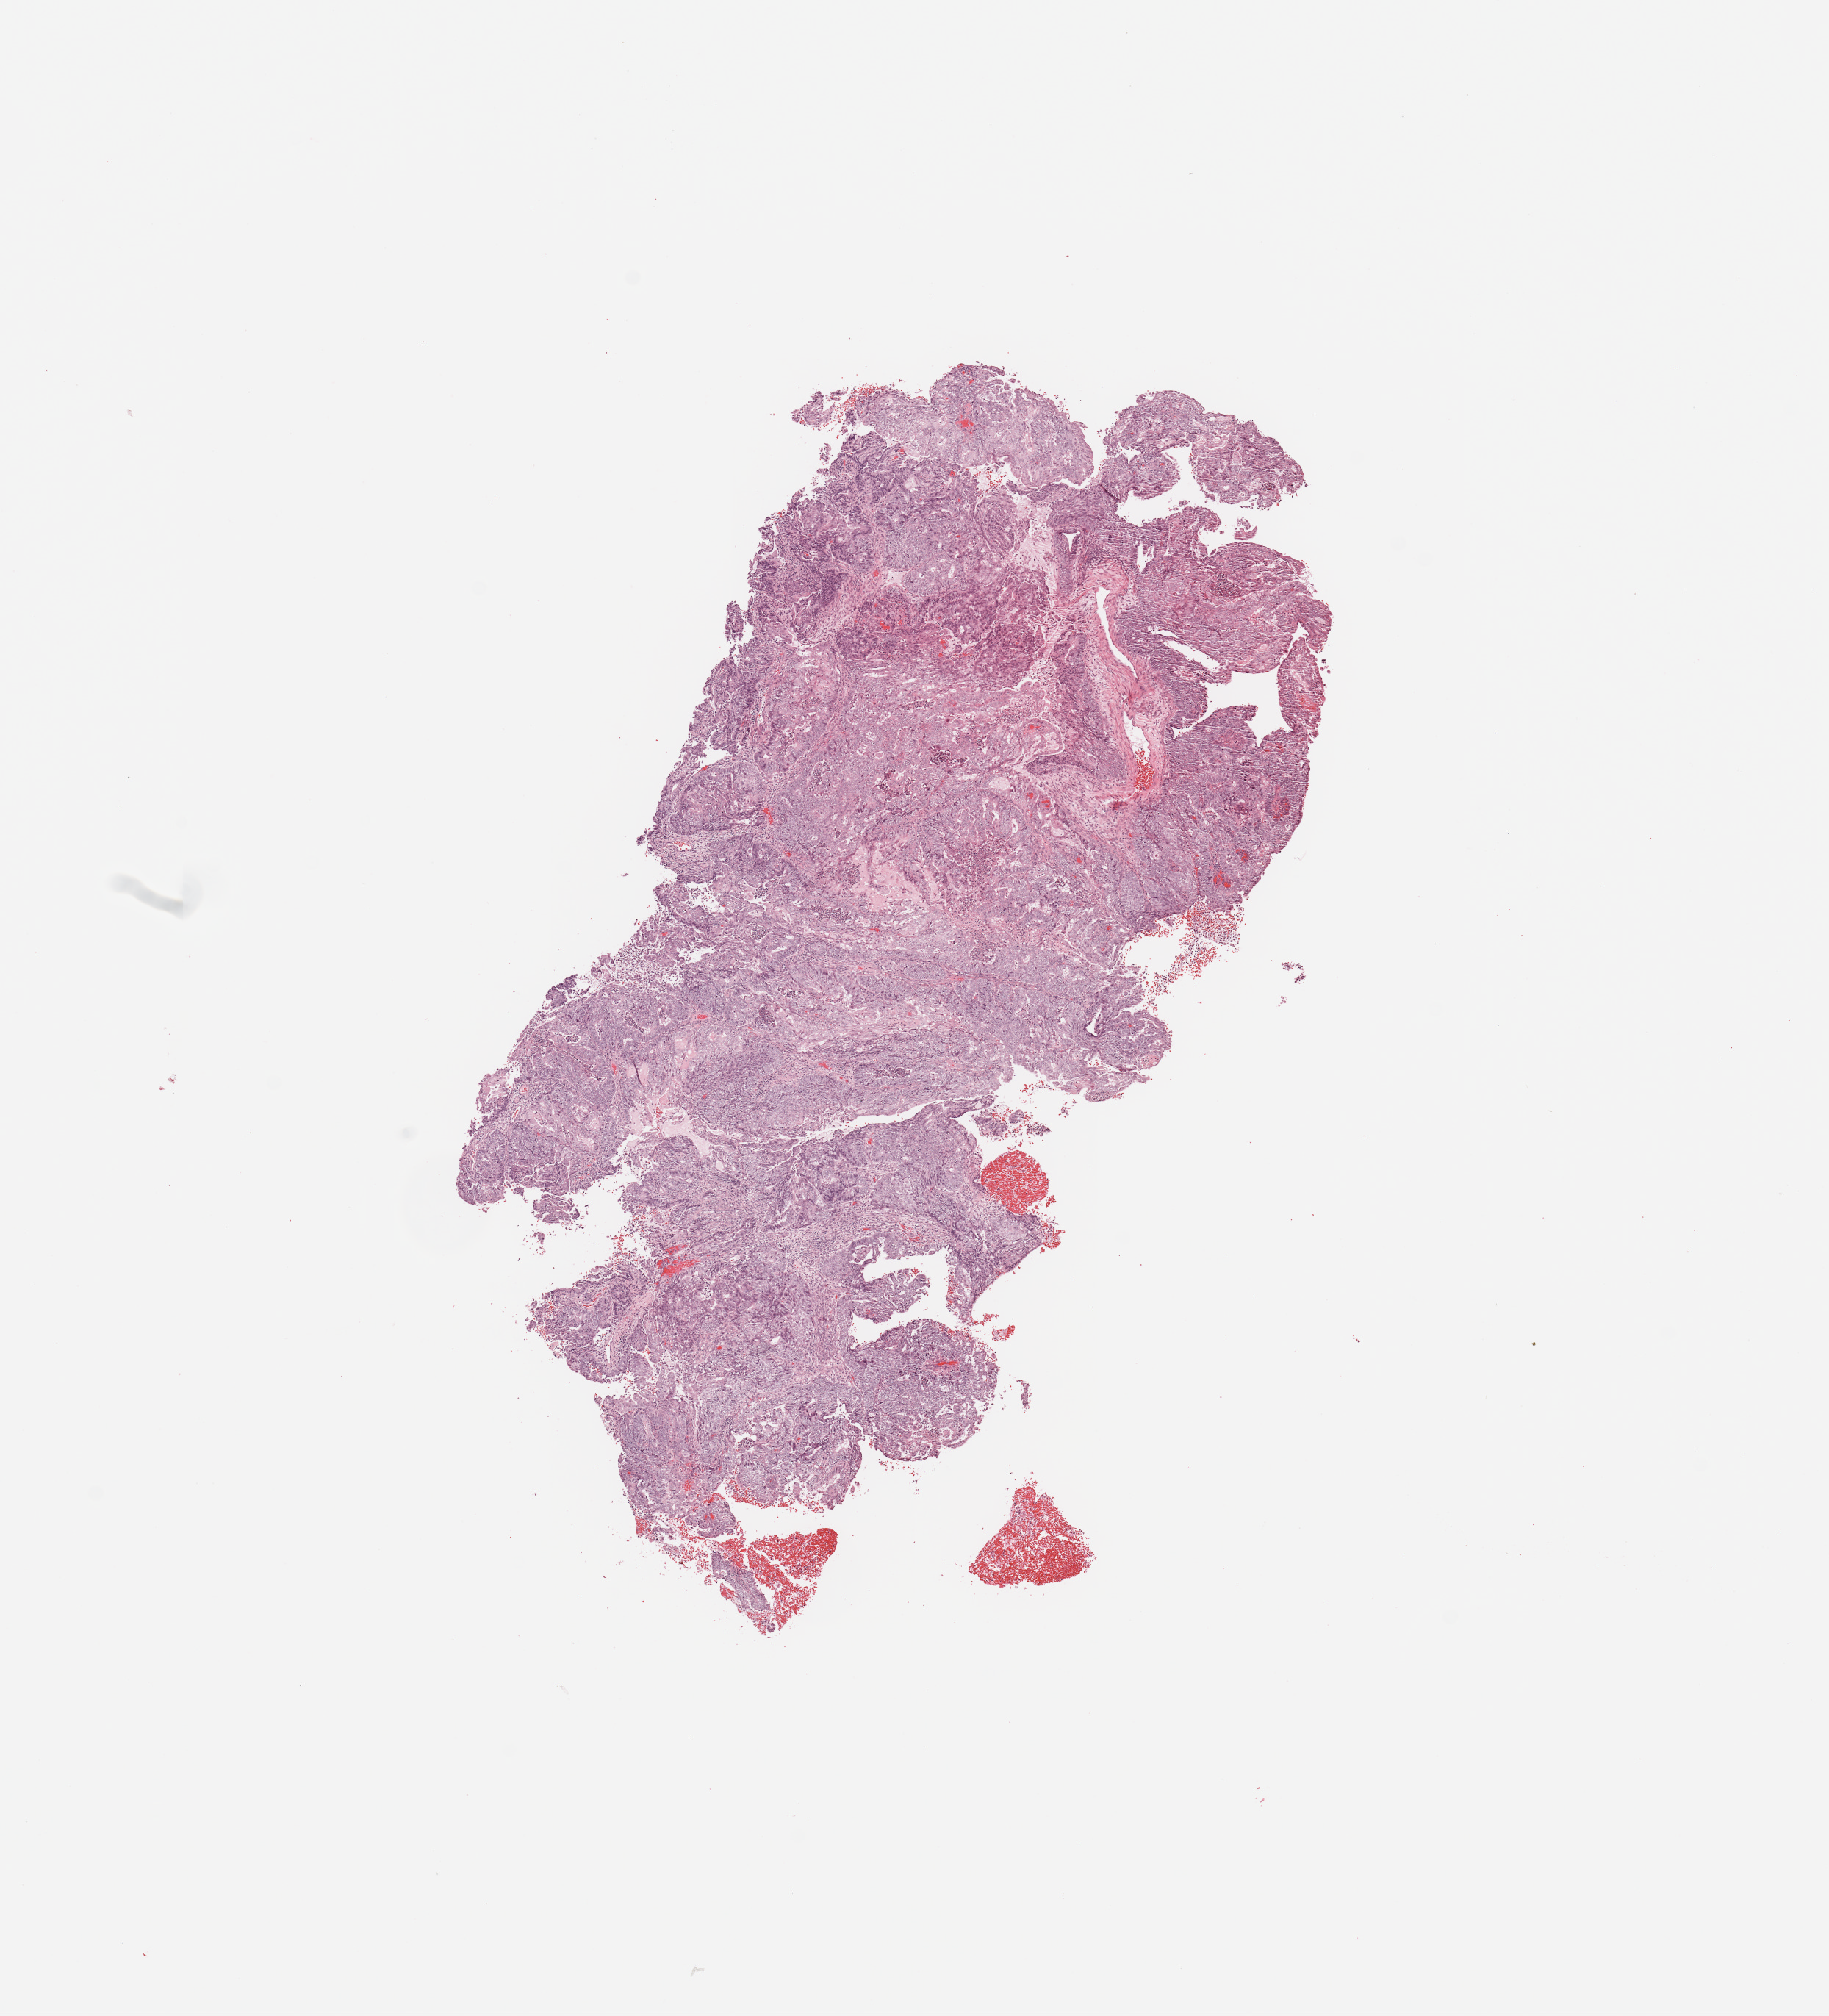
Whole-slide histology image, Hematoxylin and eosin (H&E) stained — whole scanned area (about 9.8 x 10.8 mm, slide scanned at 20x) shown as a low-resolution overview; tumour tissue sample, sampled site: uterus. 65-year-old female patient. Histologic grade: G2 (moderately differentiated). Composition of this section per pathologist review: tumour nuclei 85%, necrosis 2%.
AJCC pathologic stage: I. Histologic diagnosis: Endometrioid adenocarcinoma, NOS.